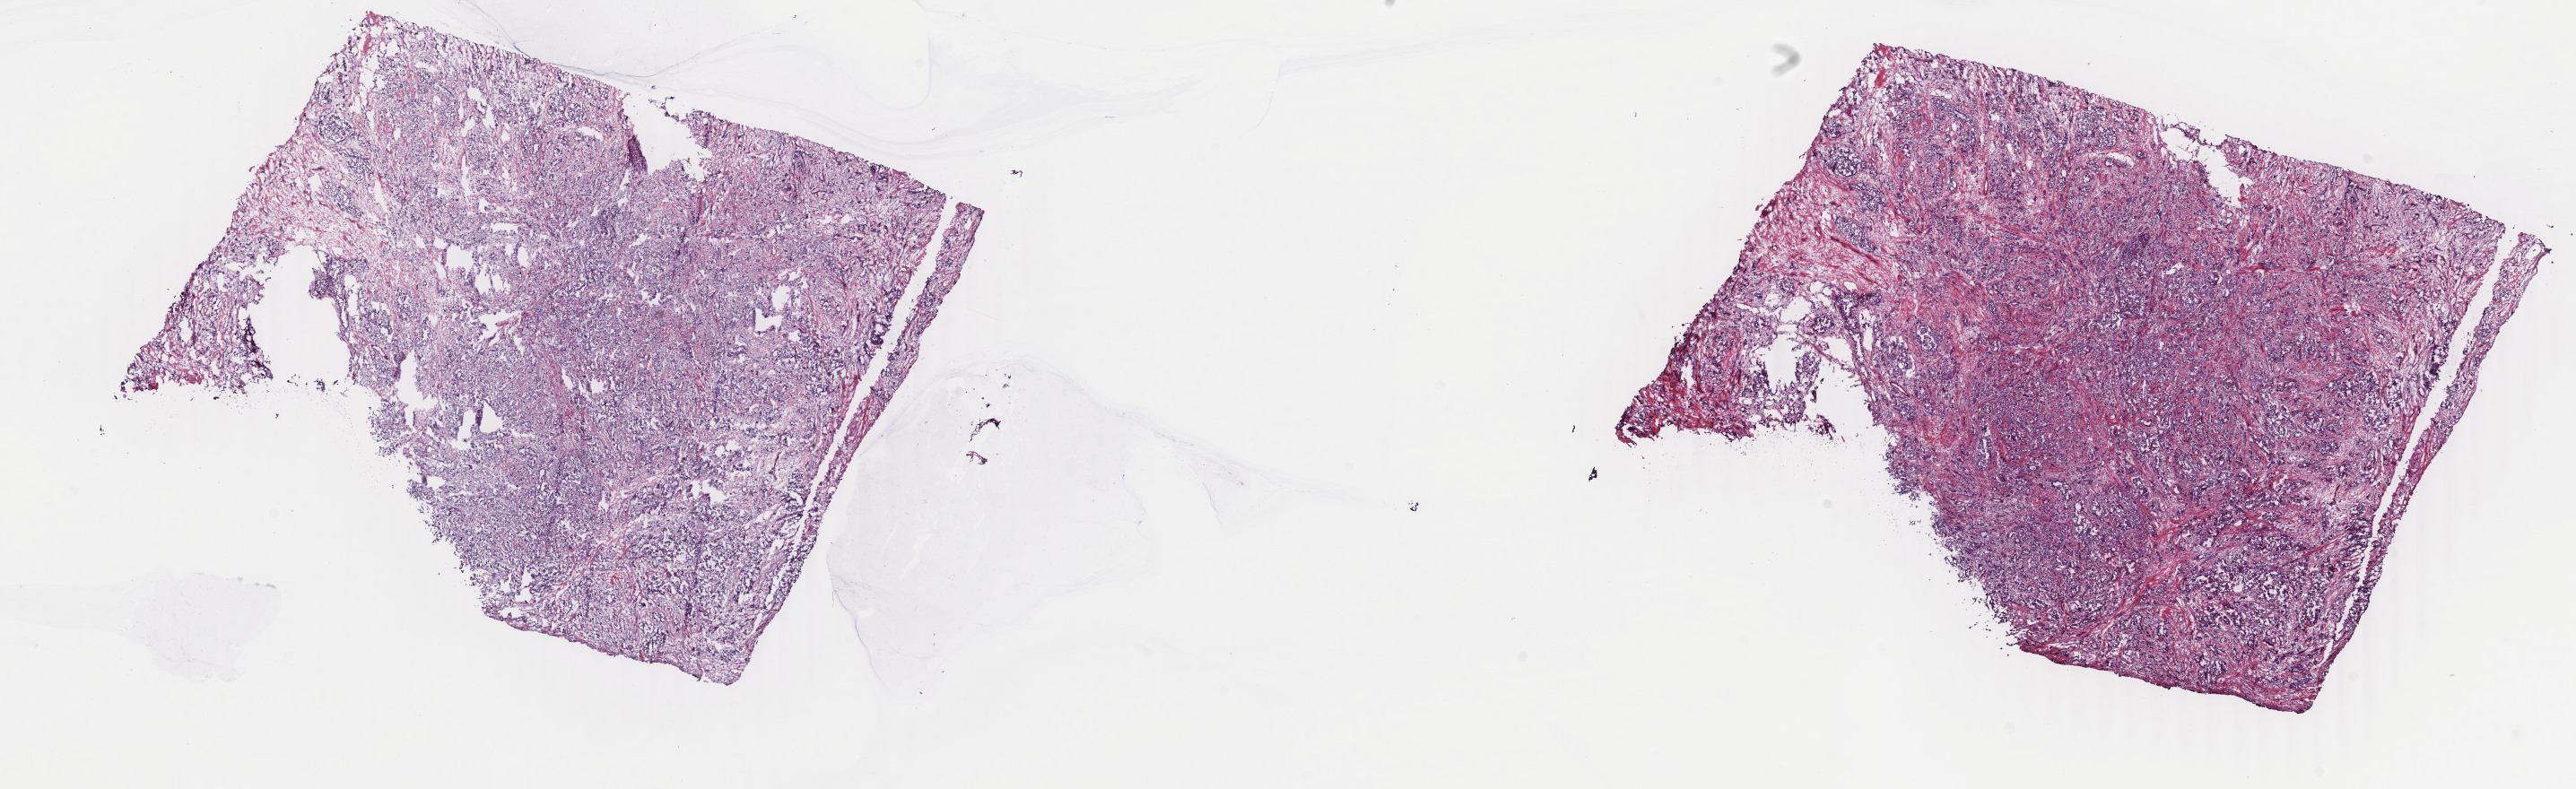
Whole-slide histology image, H&E, low-resolution overview of the scanned area, about 22.8 x 7.0 mm (acquisition: 40x scan), frozen section from the top of the tissue portion, breast, primary tumour sample. Female, age 26 years at initial diagnosis. Composition of this section per pathologist review: tumour cells 80%, tumour nuclei 80%.
Diagnosis: Infiltrating duct carcinoma, NOS.